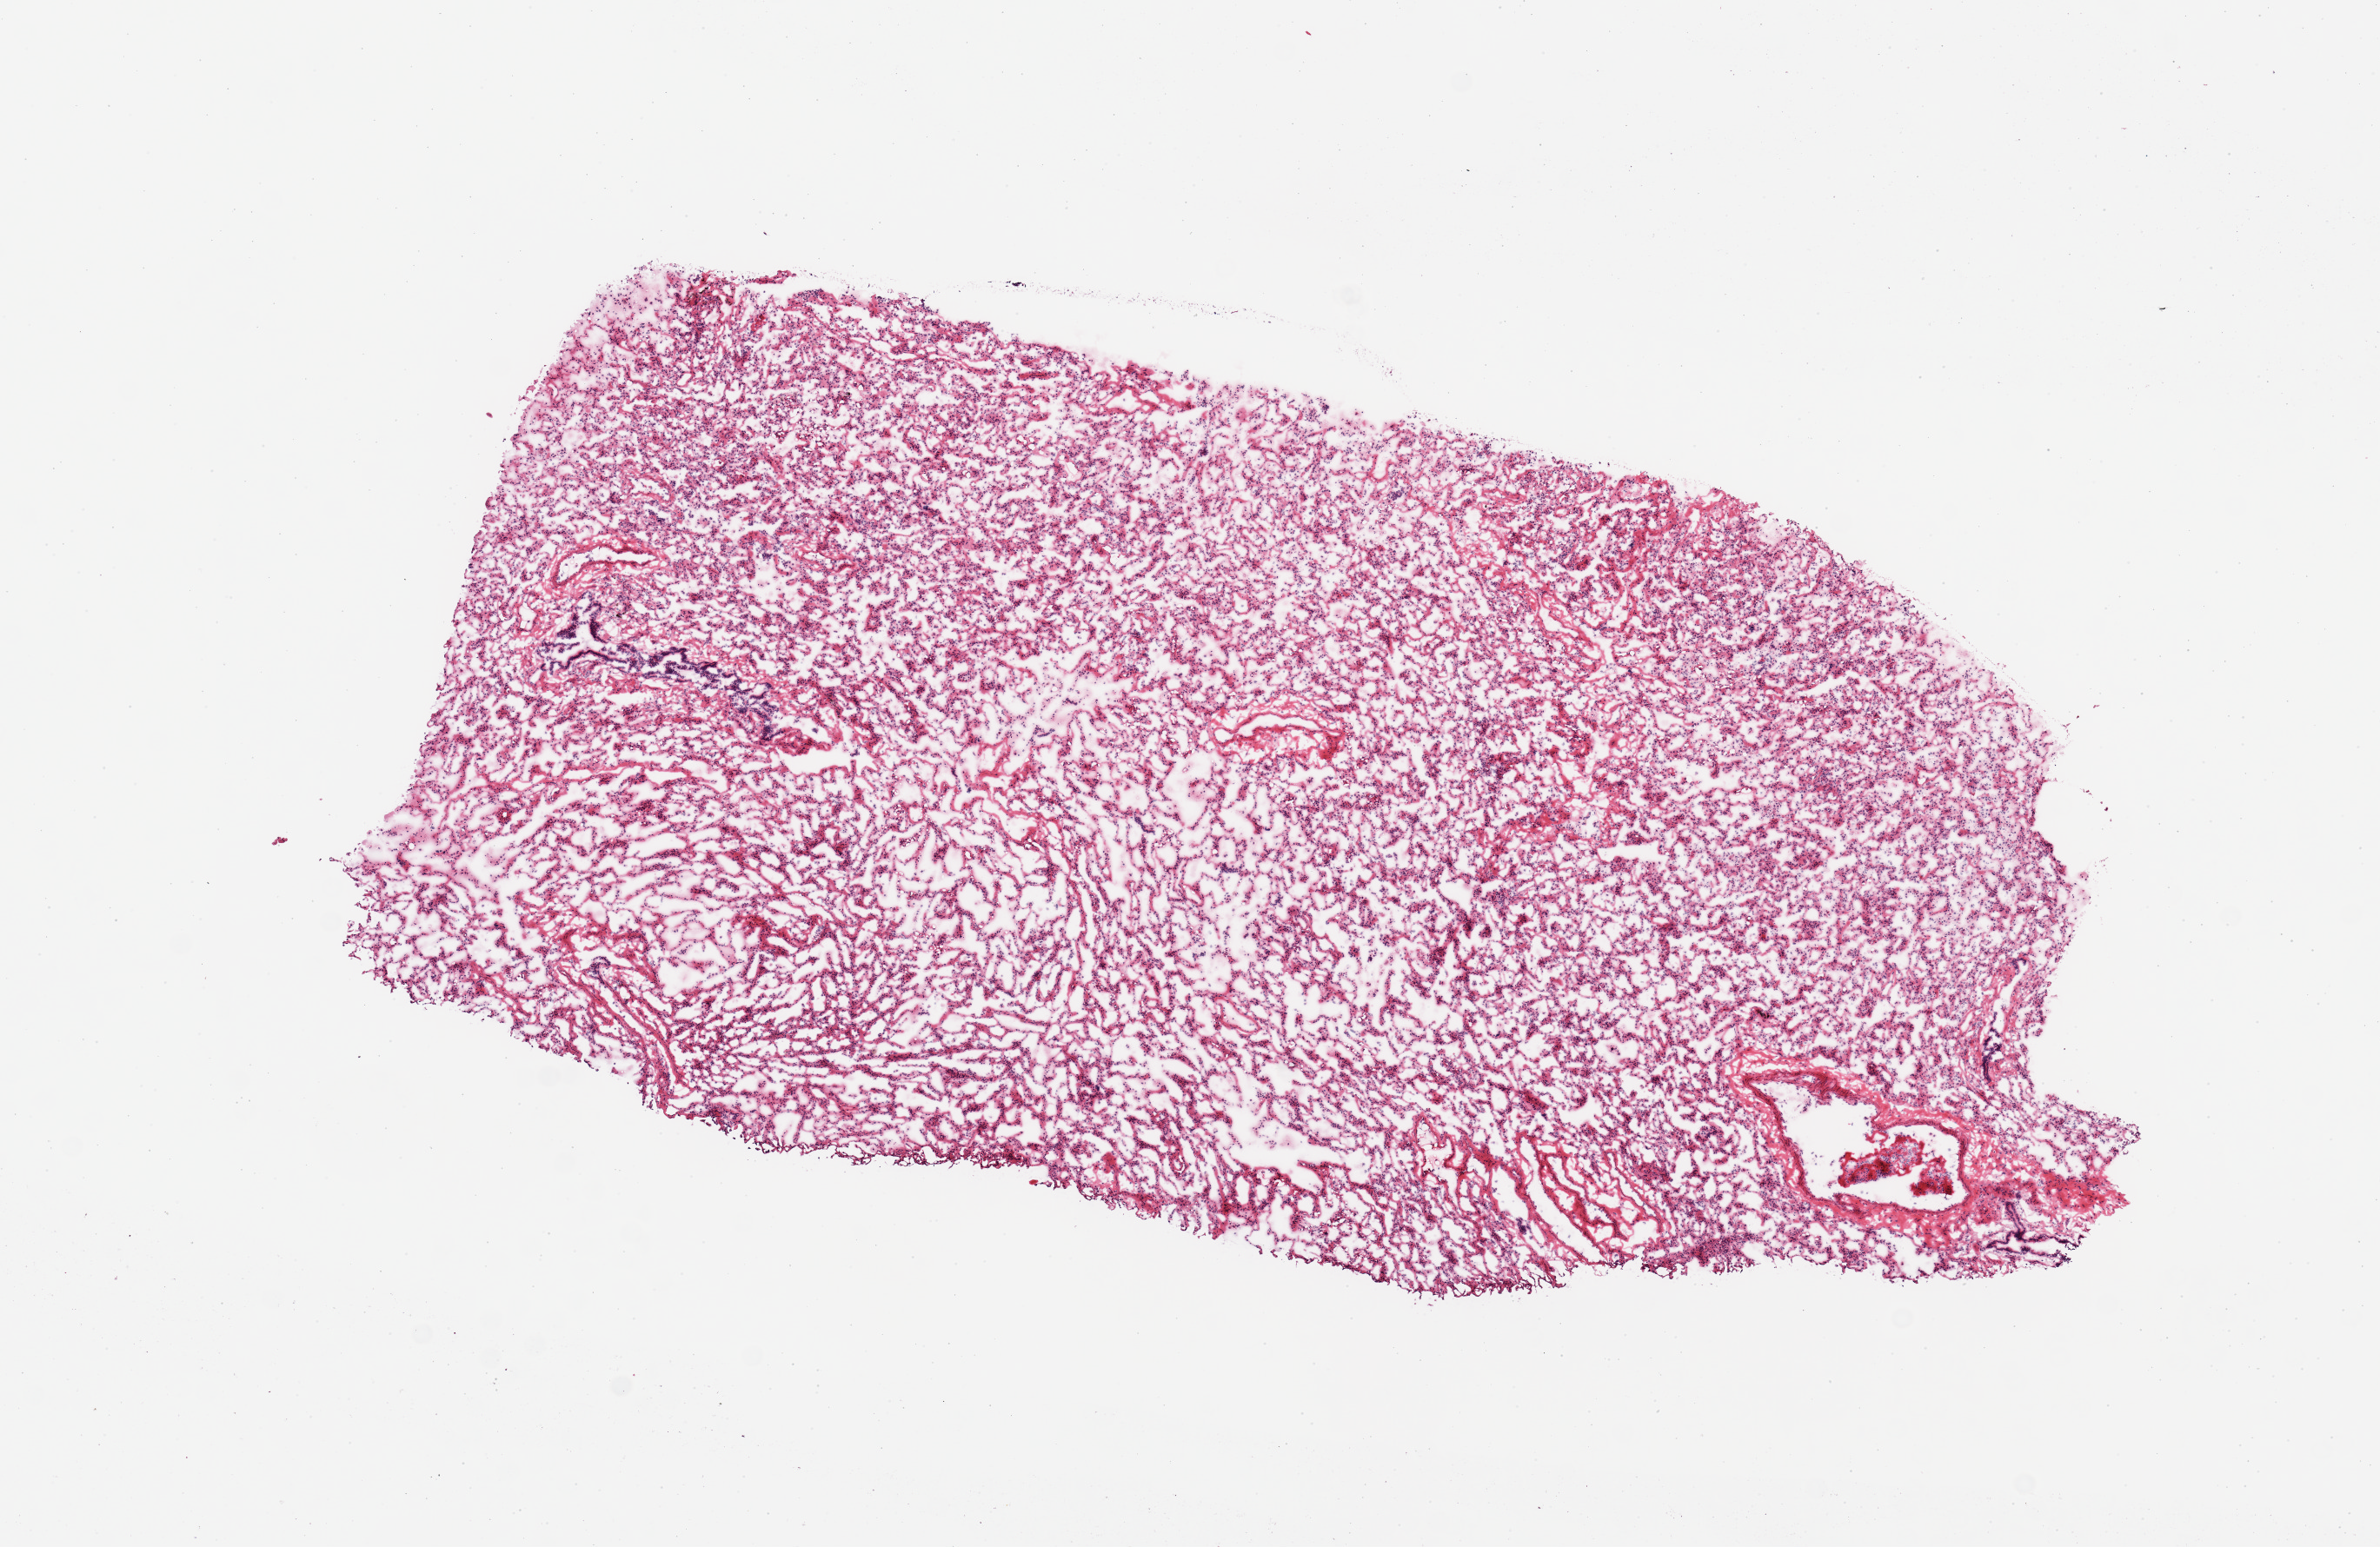
Digitized haematoxylin and eosin-stained section, shown as a low-resolution overview of the whole scanned area (about 10.8 x 7.0 mm, acquisition: 20x scan); frozen section (dry ice); section of lung (target tissue); tissue donor sample. Donor: male.
- reviewer comment on this tissue sample: 1 piece